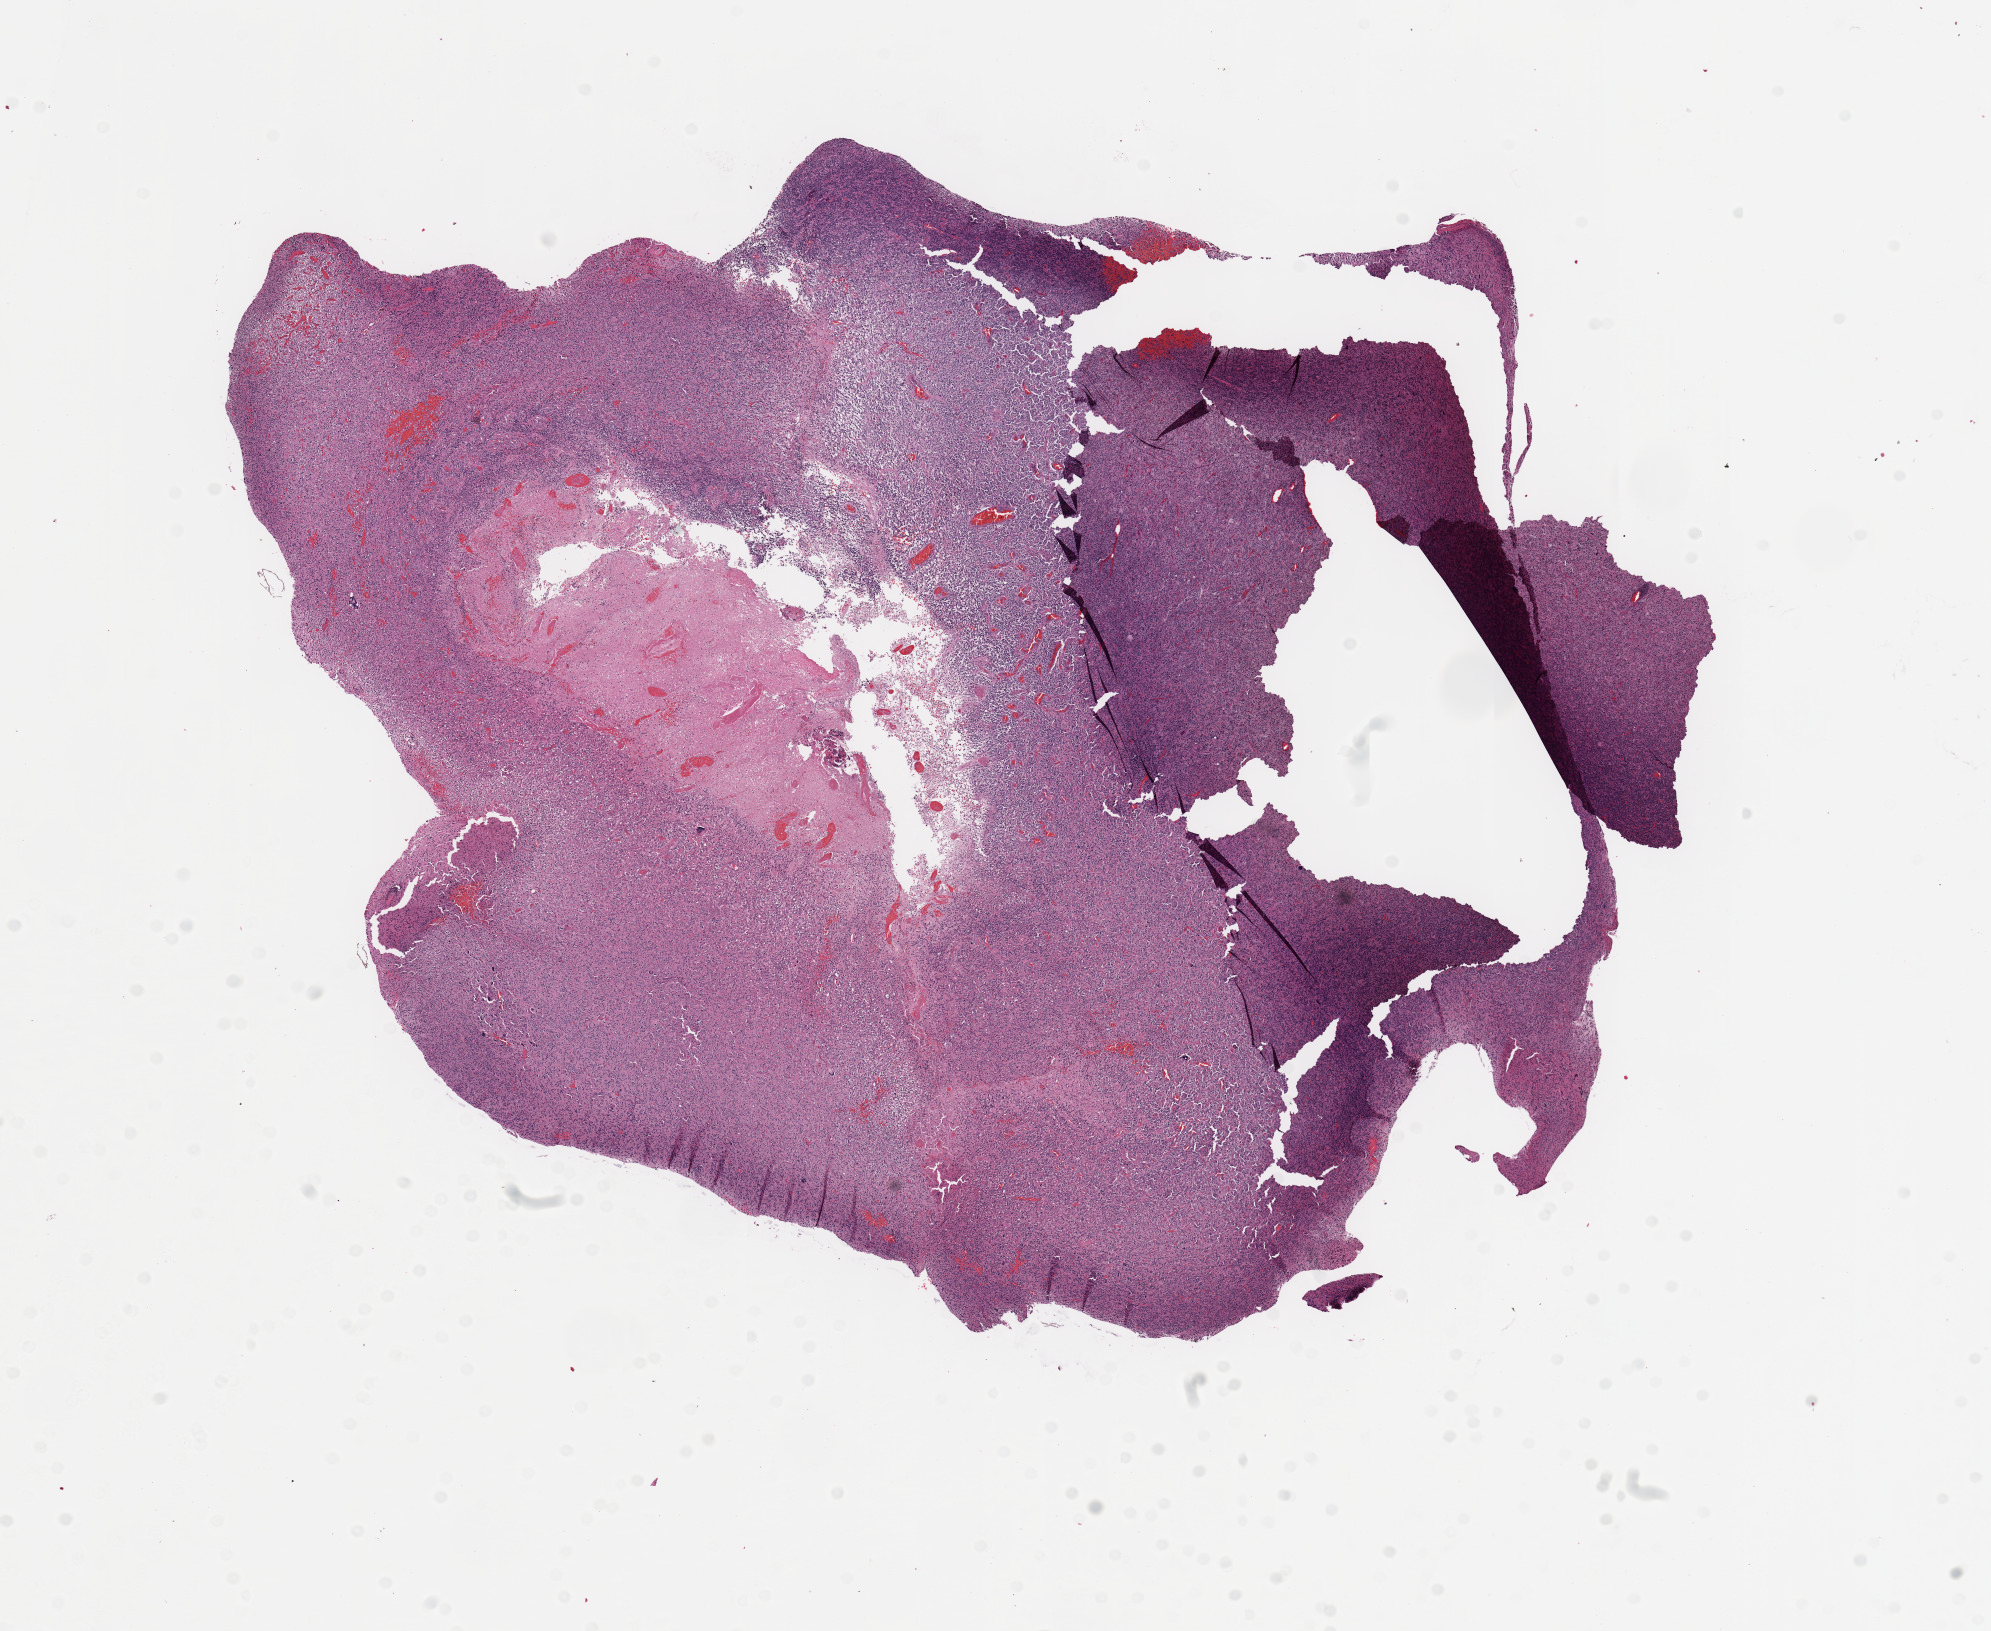
Whole-slide histology image, Hematoxylin and eosin (H&E) stained — a low-resolution overview of the entire scanned area, about 15.8 x 12.9 mm (slide scanned at 20x); tumour tissue sample, sampled site: brain. 59-year-old male patient. Slide review estimates, as recorded: tumour nuclei 85%, necrosis 15%.
Histologic diagnosis: Glioblastoma.